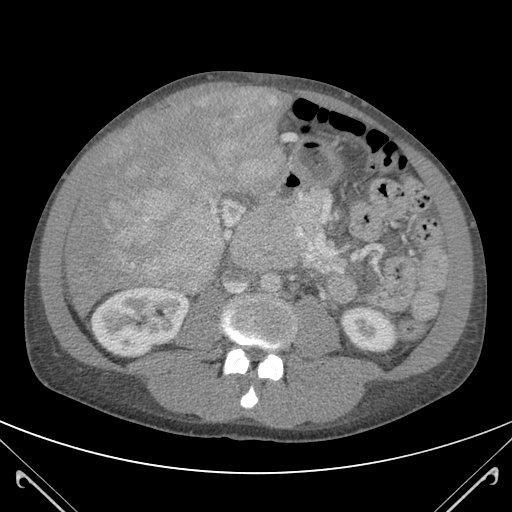
Contrast-enhanced abdominal CT (liver protocol), one axial slice; slice 43 of 118 in the series (ordered by position); 120 kVp; soft-tissue window (W 400 / L 40 HU); 3 mm slice thickness; 512 × 512 image matrix, field of view 380 × 380 mm. Case-level facts recorded for this patient, not image findings: diagnosis: hepatocellular carcinoma (patient treated with transarterial chemoembolisation; whether this scan precedes or follows treatment is not stated here); TNM stage (as recorded): Stage-IIIB; Child-Pugh class: A.
Annotated regions visible in this slice (semi-automatically segmented with operator editing):
- abdominal aorta: bounding box (x1, y1, x2, y2) in pixels: (261, 273, 280, 295)
- liver parenchyma outside the tumour (the mass and vessels are separate outlines, so this box may not span the whole liver): (66, 88, 283, 311)
- mass: (93, 88, 286, 287)